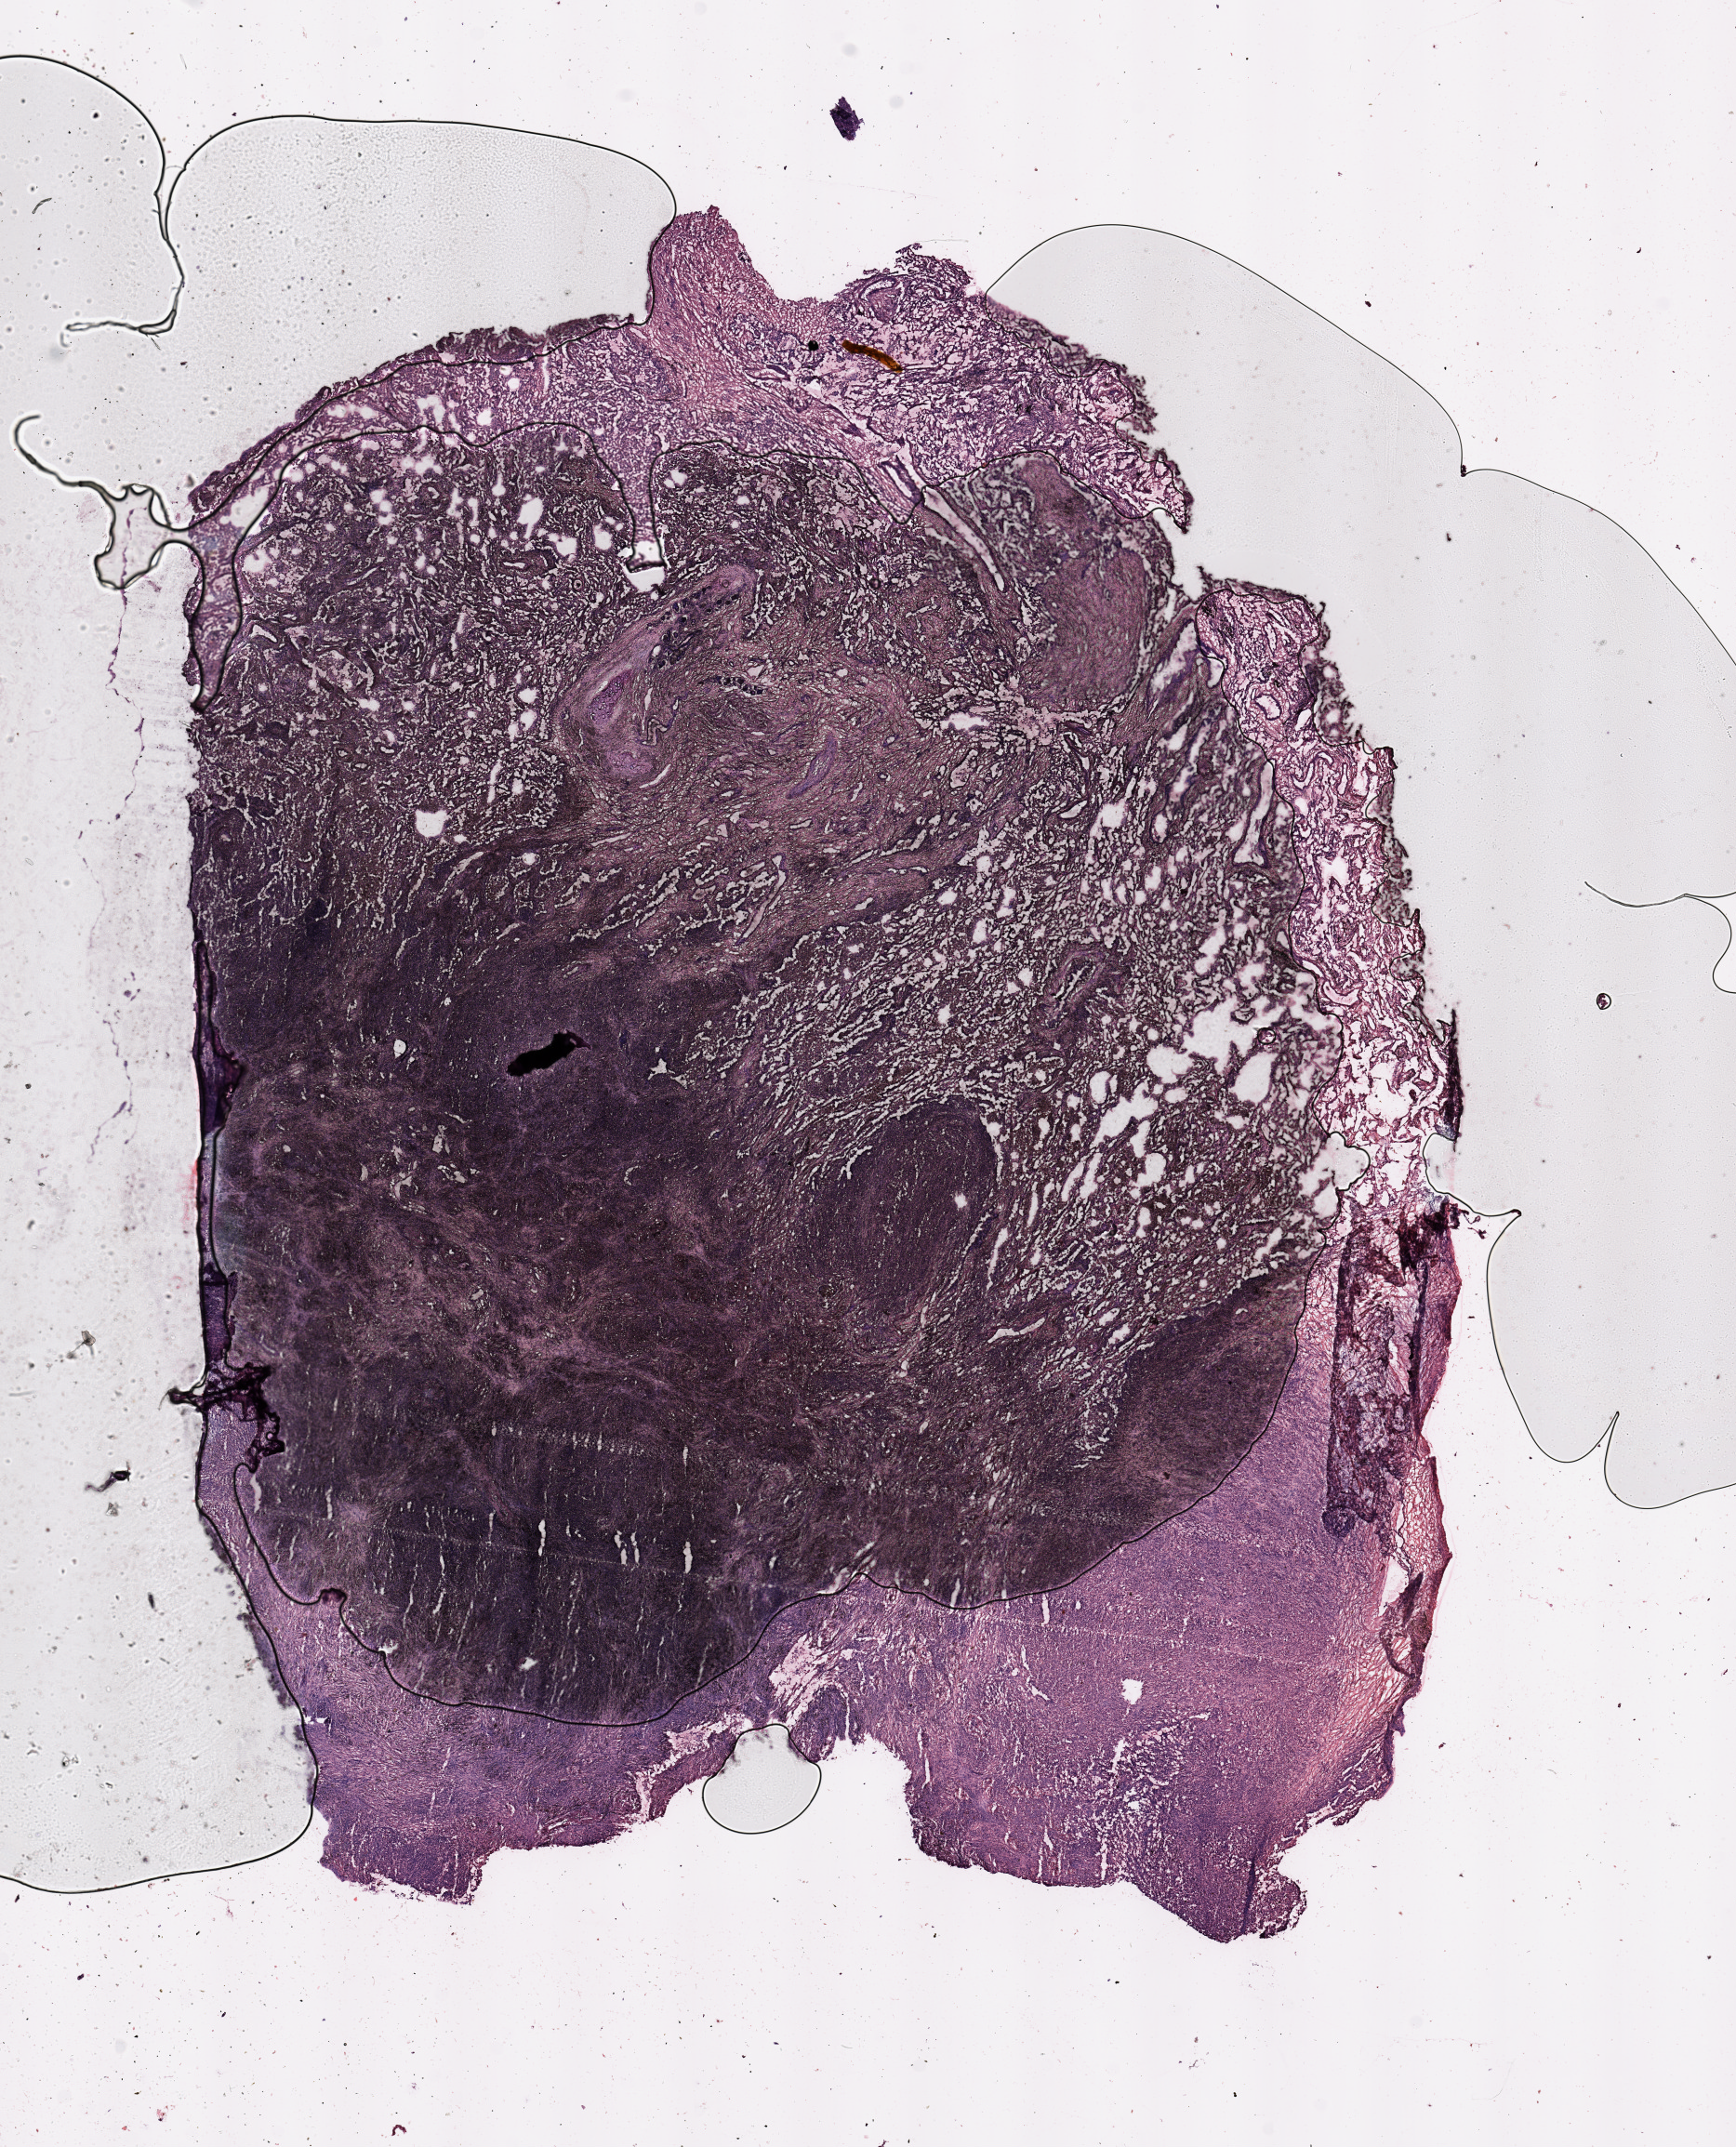
Digitized H&E-stained tissue section (whole slide) — a low-resolution overview of the entire scanned area, about 14.8 x 18.3 mm. Tumour tissue sample, lung. 57-year-old male patient. Histologic grade: G3 (poorly differentiated).
AJCC pathologic stage: IB. Primary tumour site (as recorded): right upper lobe. Histologic diagnosis: Adenocarcinoma, NOS.